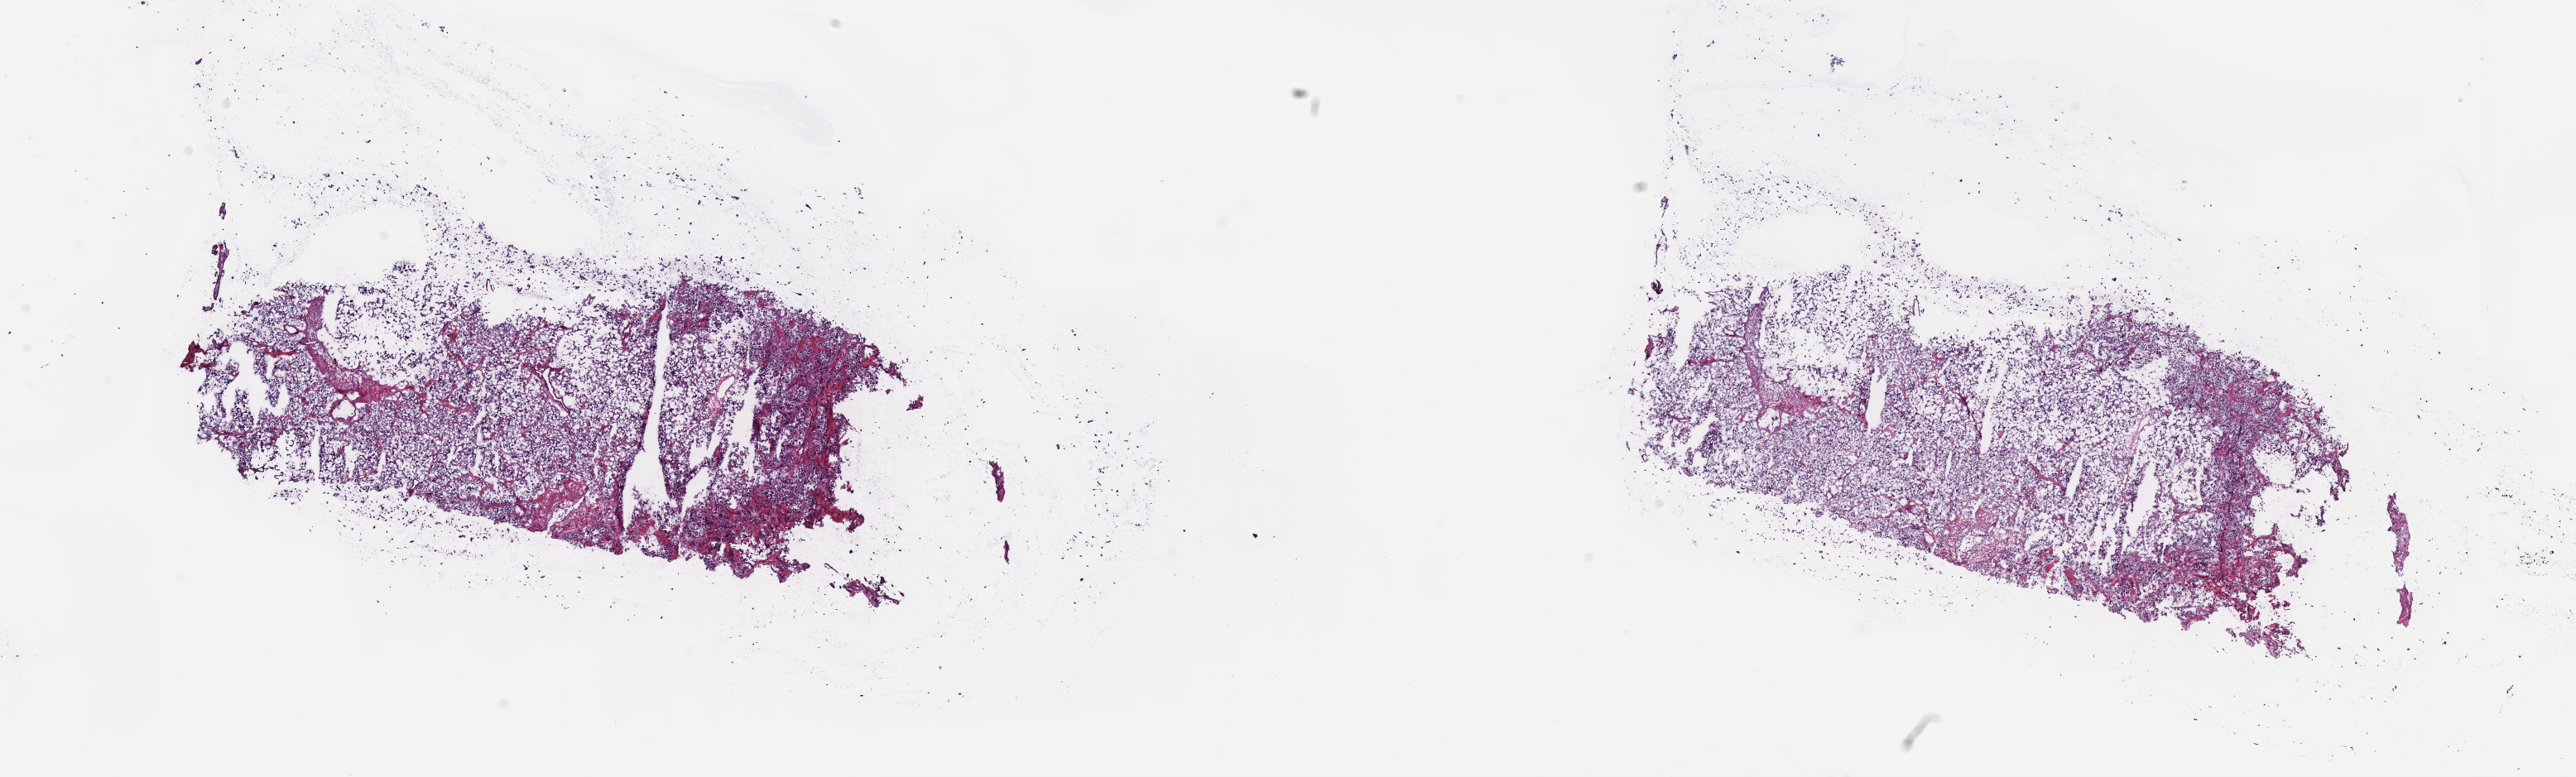
H&E whole-slide image, a low-resolution overview of the entire scanned area, about 25.2 x 7.6 mm (from a 40x scan); frozen section; sample: primary tumour, adrenal gland. Female, age 59 years at initial diagnosis. Slide review estimates, as recorded: tumour cells 100%, tumour nuclei 75%, normal cells 0%, stromal cells 0%, necrosis 0%. Infiltration values recorded for this section: lymphocyte infiltration 1%, monocyte infiltration 0%, neutrophil infiltration 0%.
• diagnosis: Pheochromocytoma, NOS